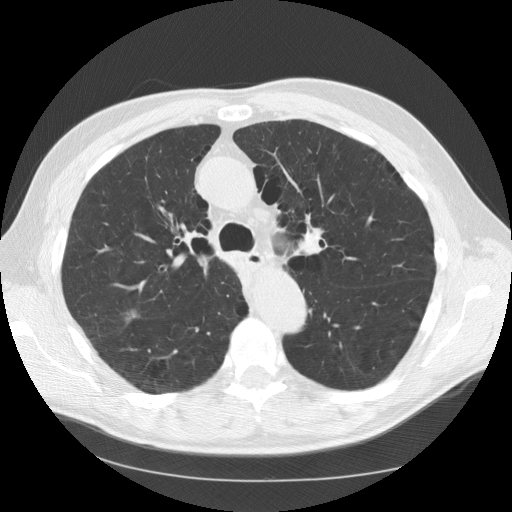
Low-dose screening chest CT, one axial slice. Slice 87 of 133 in the series (ordered by position). Reconstruction kernel STANDARD. Lung window (W 1500 / L -600 HU). 2.5 mm slice thickness. 512 × 512 image matrix, field of view 377 × 377 mm.
Annotated regions visible in this slice (expert manual segmentation):
- lesion 1 (tumor, upper lobe of right lung): box from (x=126, y=312) to (x=136, y=320) px